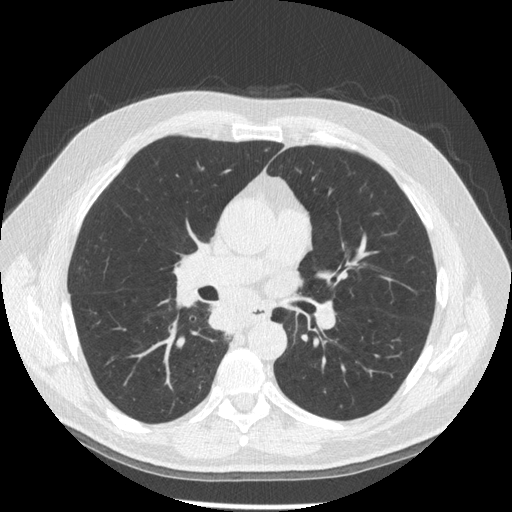
Chest CT (low-dose screening protocol), one axial image. Third annual screen. Lung window (W 1500 / L -600 HU). Standard (soft-tissue) reconstruction kernel (STANDARD). Slice 80 of 181 in the series. 512 × 512 image matrix, field of view 370 × 370 mm. Male, age 61 years at enrolment. Former smoker at enrolment.
• Expert reader's lesion annotation, bounding box (x1, y1, x2, y2) in pixels: (206, 298, 255, 345).
• No non-calcified nodule or mass ≥4 mm was recorded by the screening reader at this exam.
• Lung cancer was diagnosed 10 days after this screen: squamous cell carcinoma, keratinizing, NOS, right lower lobe, stage IIIB (AJCC 6th edition), 40 mm at pathology.